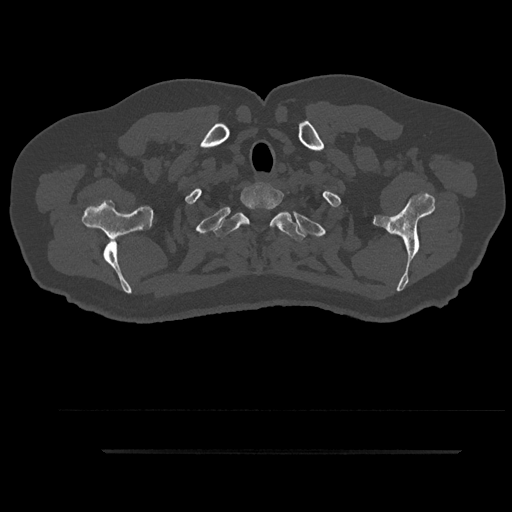
CT including the spine, one axial slice. Slice 777 of 797 in the series (ordered by position). Reconstruction kernel Br40s/3. 120 kVp. Bone window (W 1800 / L 400 HU). 0.5 mm slice thickness. 512 × 512 image matrix, field of view 432 × 432 mm. Patient: male, 63 years. From the clinical record (not read from this slice): primary cancer: renal.
Outlined on this slice (semi-automatically segmented with operator editing):
- T1 vertebra: bounding box (x1, y1, x2, y2) in pixels: (240, 185, 290, 226)
- T2 vertebra: (213, 207, 306, 241)